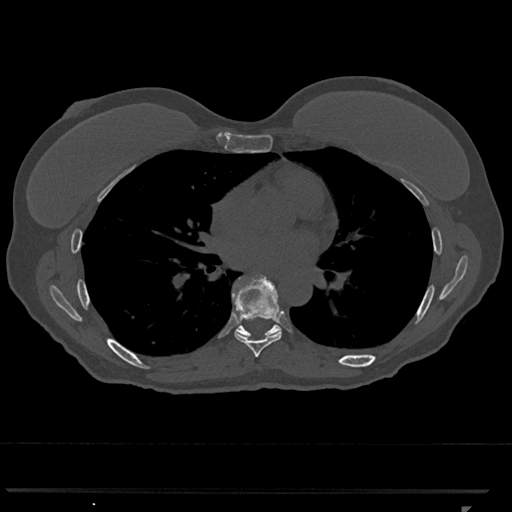
CT including the spine, one axial slice. Position 698 of 793 along the scan axis. Reconstruction kernel Br40s/3. 120 kVp. Bone window (W 1800 / L 400 HU). 512 × 512 image matrix, field of view 380 × 380 mm. Patient: female, 62 years. From the clinical record (not read from this slice): primary cancer: renal.
Annotated regions visible in this slice (semi-automatic segmentation, software-assisted and operator-edited):
- T7 vertebra: box from (x=233, y=276) to (x=282, y=357) px
- T8 vertebra: (x=233, y=277)–(x=280, y=337)